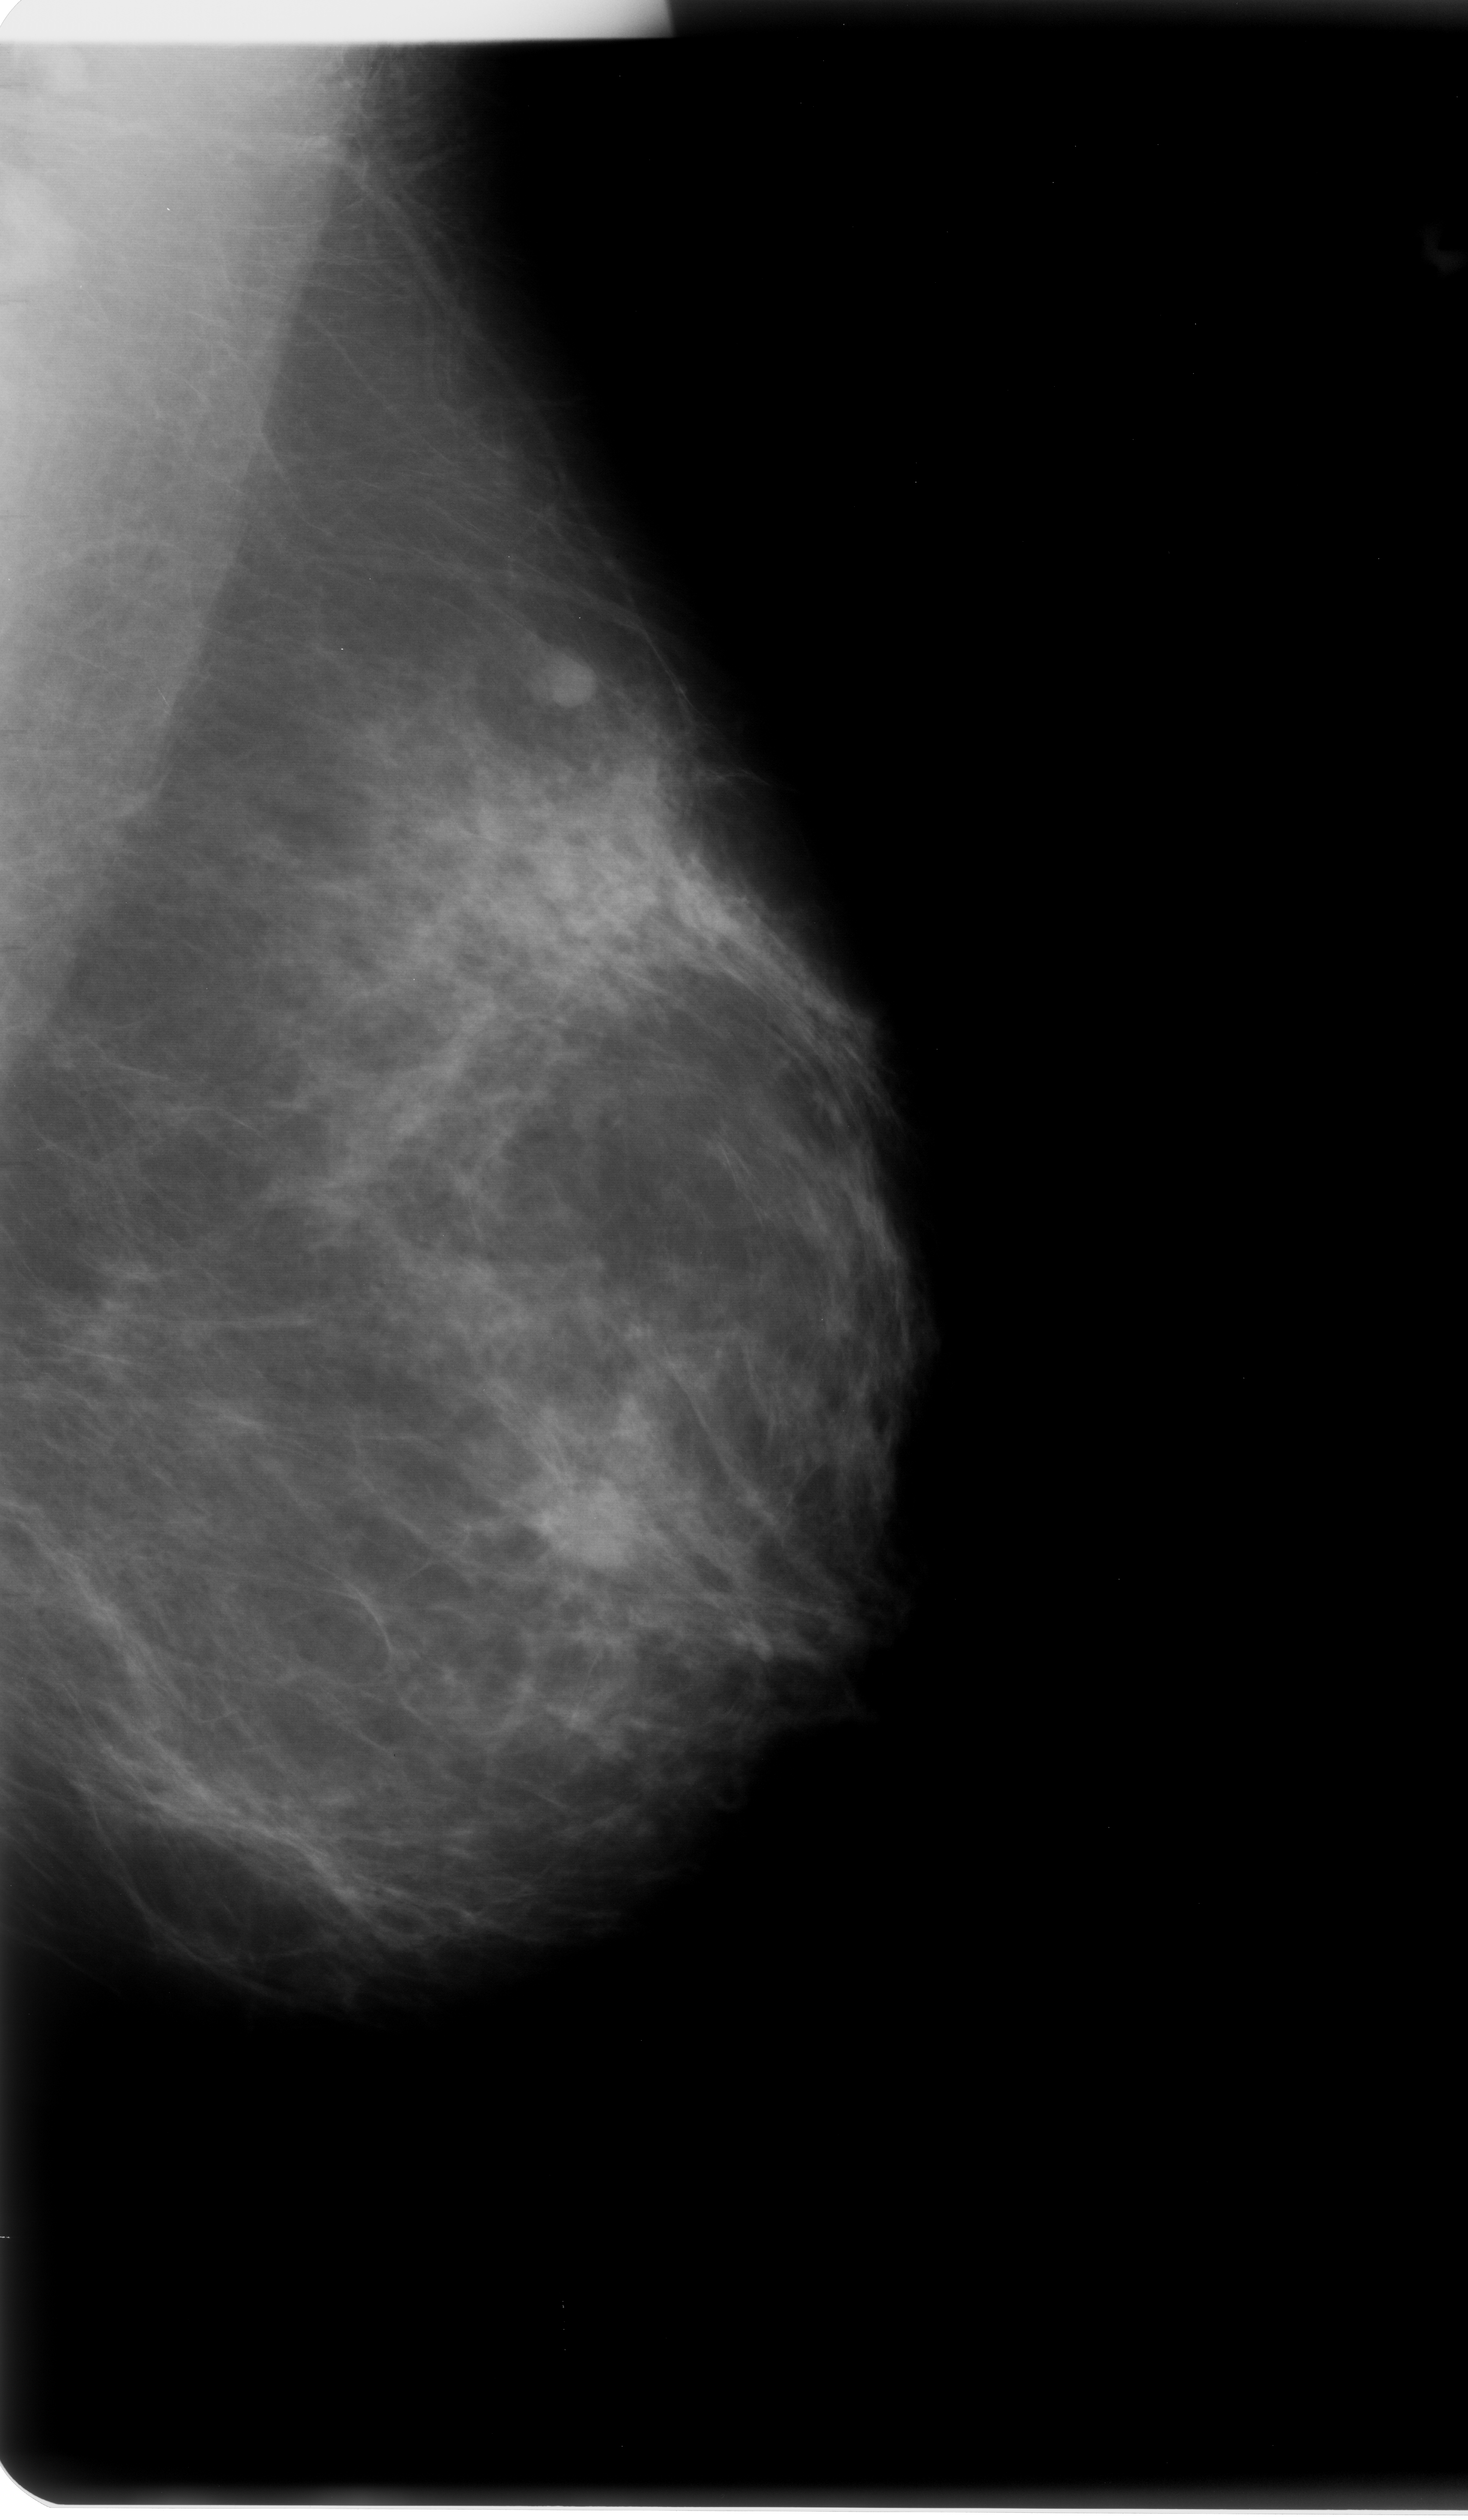
Mammogram (digitized film); left breast; mediolateral oblique (MLO) view.
Marked findings (only marked abnormalities are described; nothing is implied about the rest of the image): mass, shape round, margins spiculated; BI-RADS assessment category 5; subtlety rating 5 on a 1 (subtle) to 5 (obvious) scale; pathology result (as recorded, not read from the image): malignant.